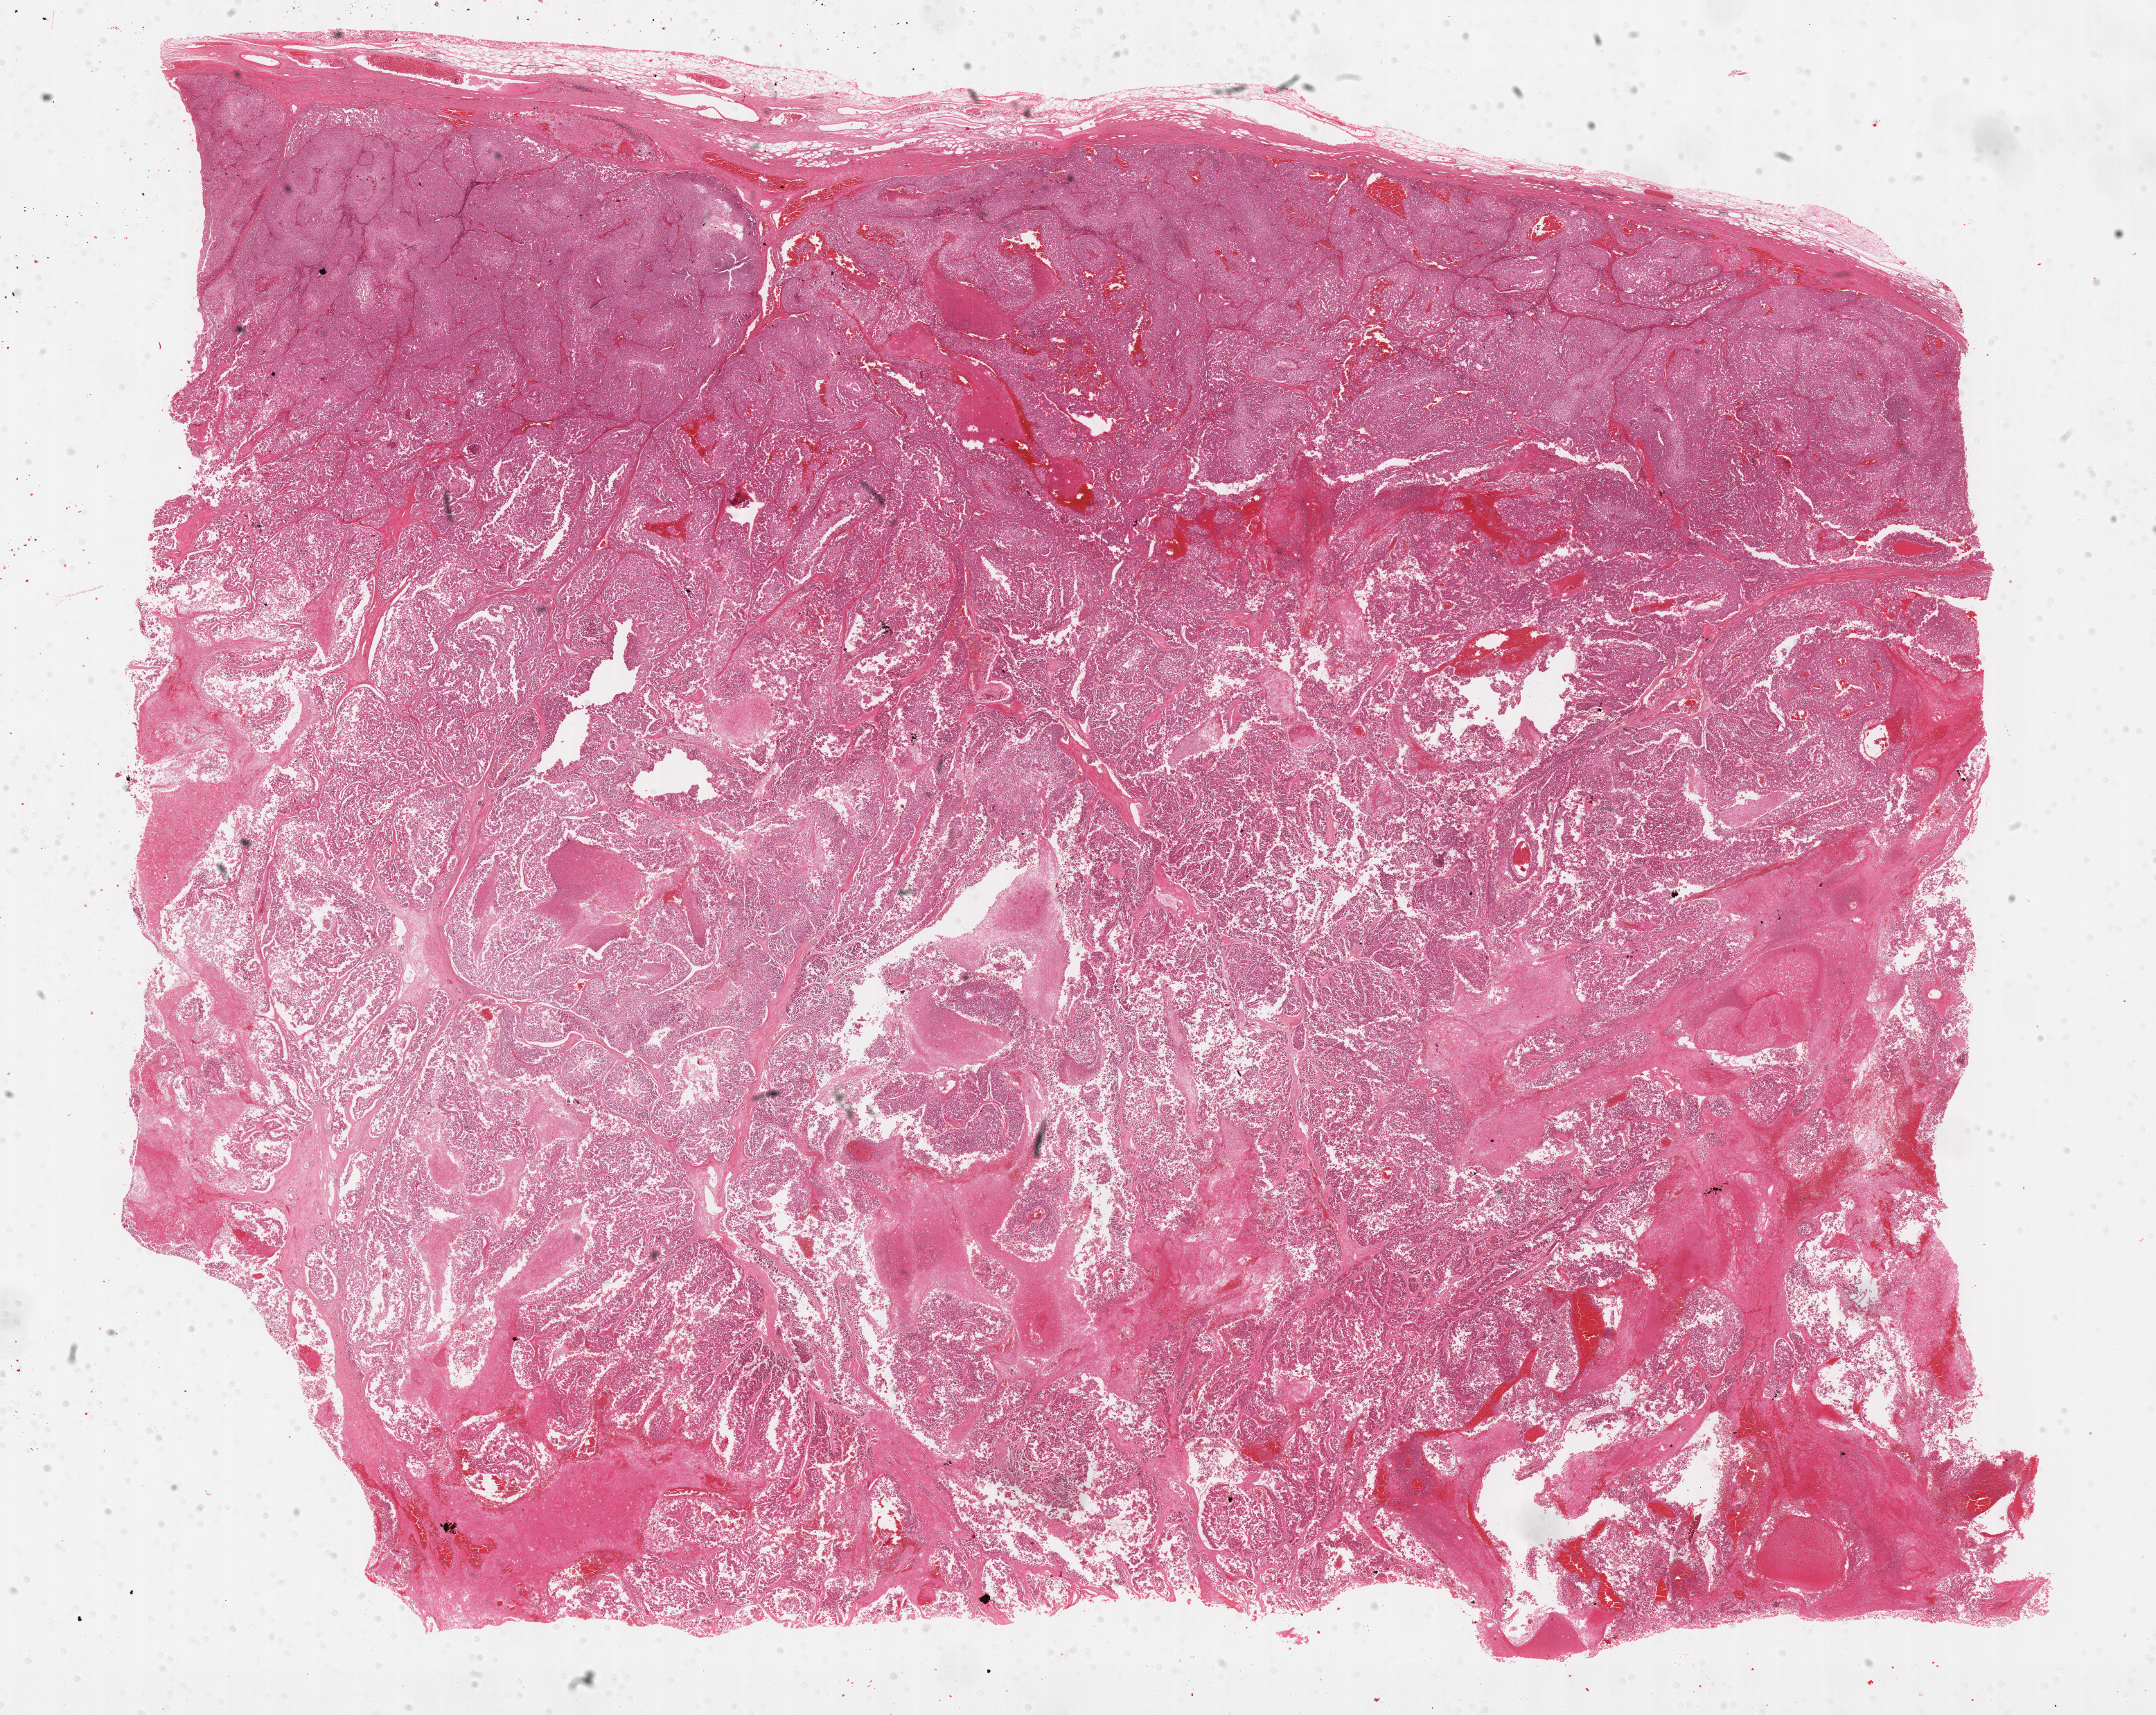
H&E whole-slide image — a low-resolution overview of the entire scanned area, about 25.2 x 20.0 mm (acquisition: 40x scan). FFPE section. Primary tumour sample from the adrenal cortex. Patient: male, age at initial diagnosis 65 years.
Lymph nodes positive (case pathology): 6 of 6 examined. Laterality: left. Diagnosis: Adrenal cortical carcinoma (cortex of adrenal gland).